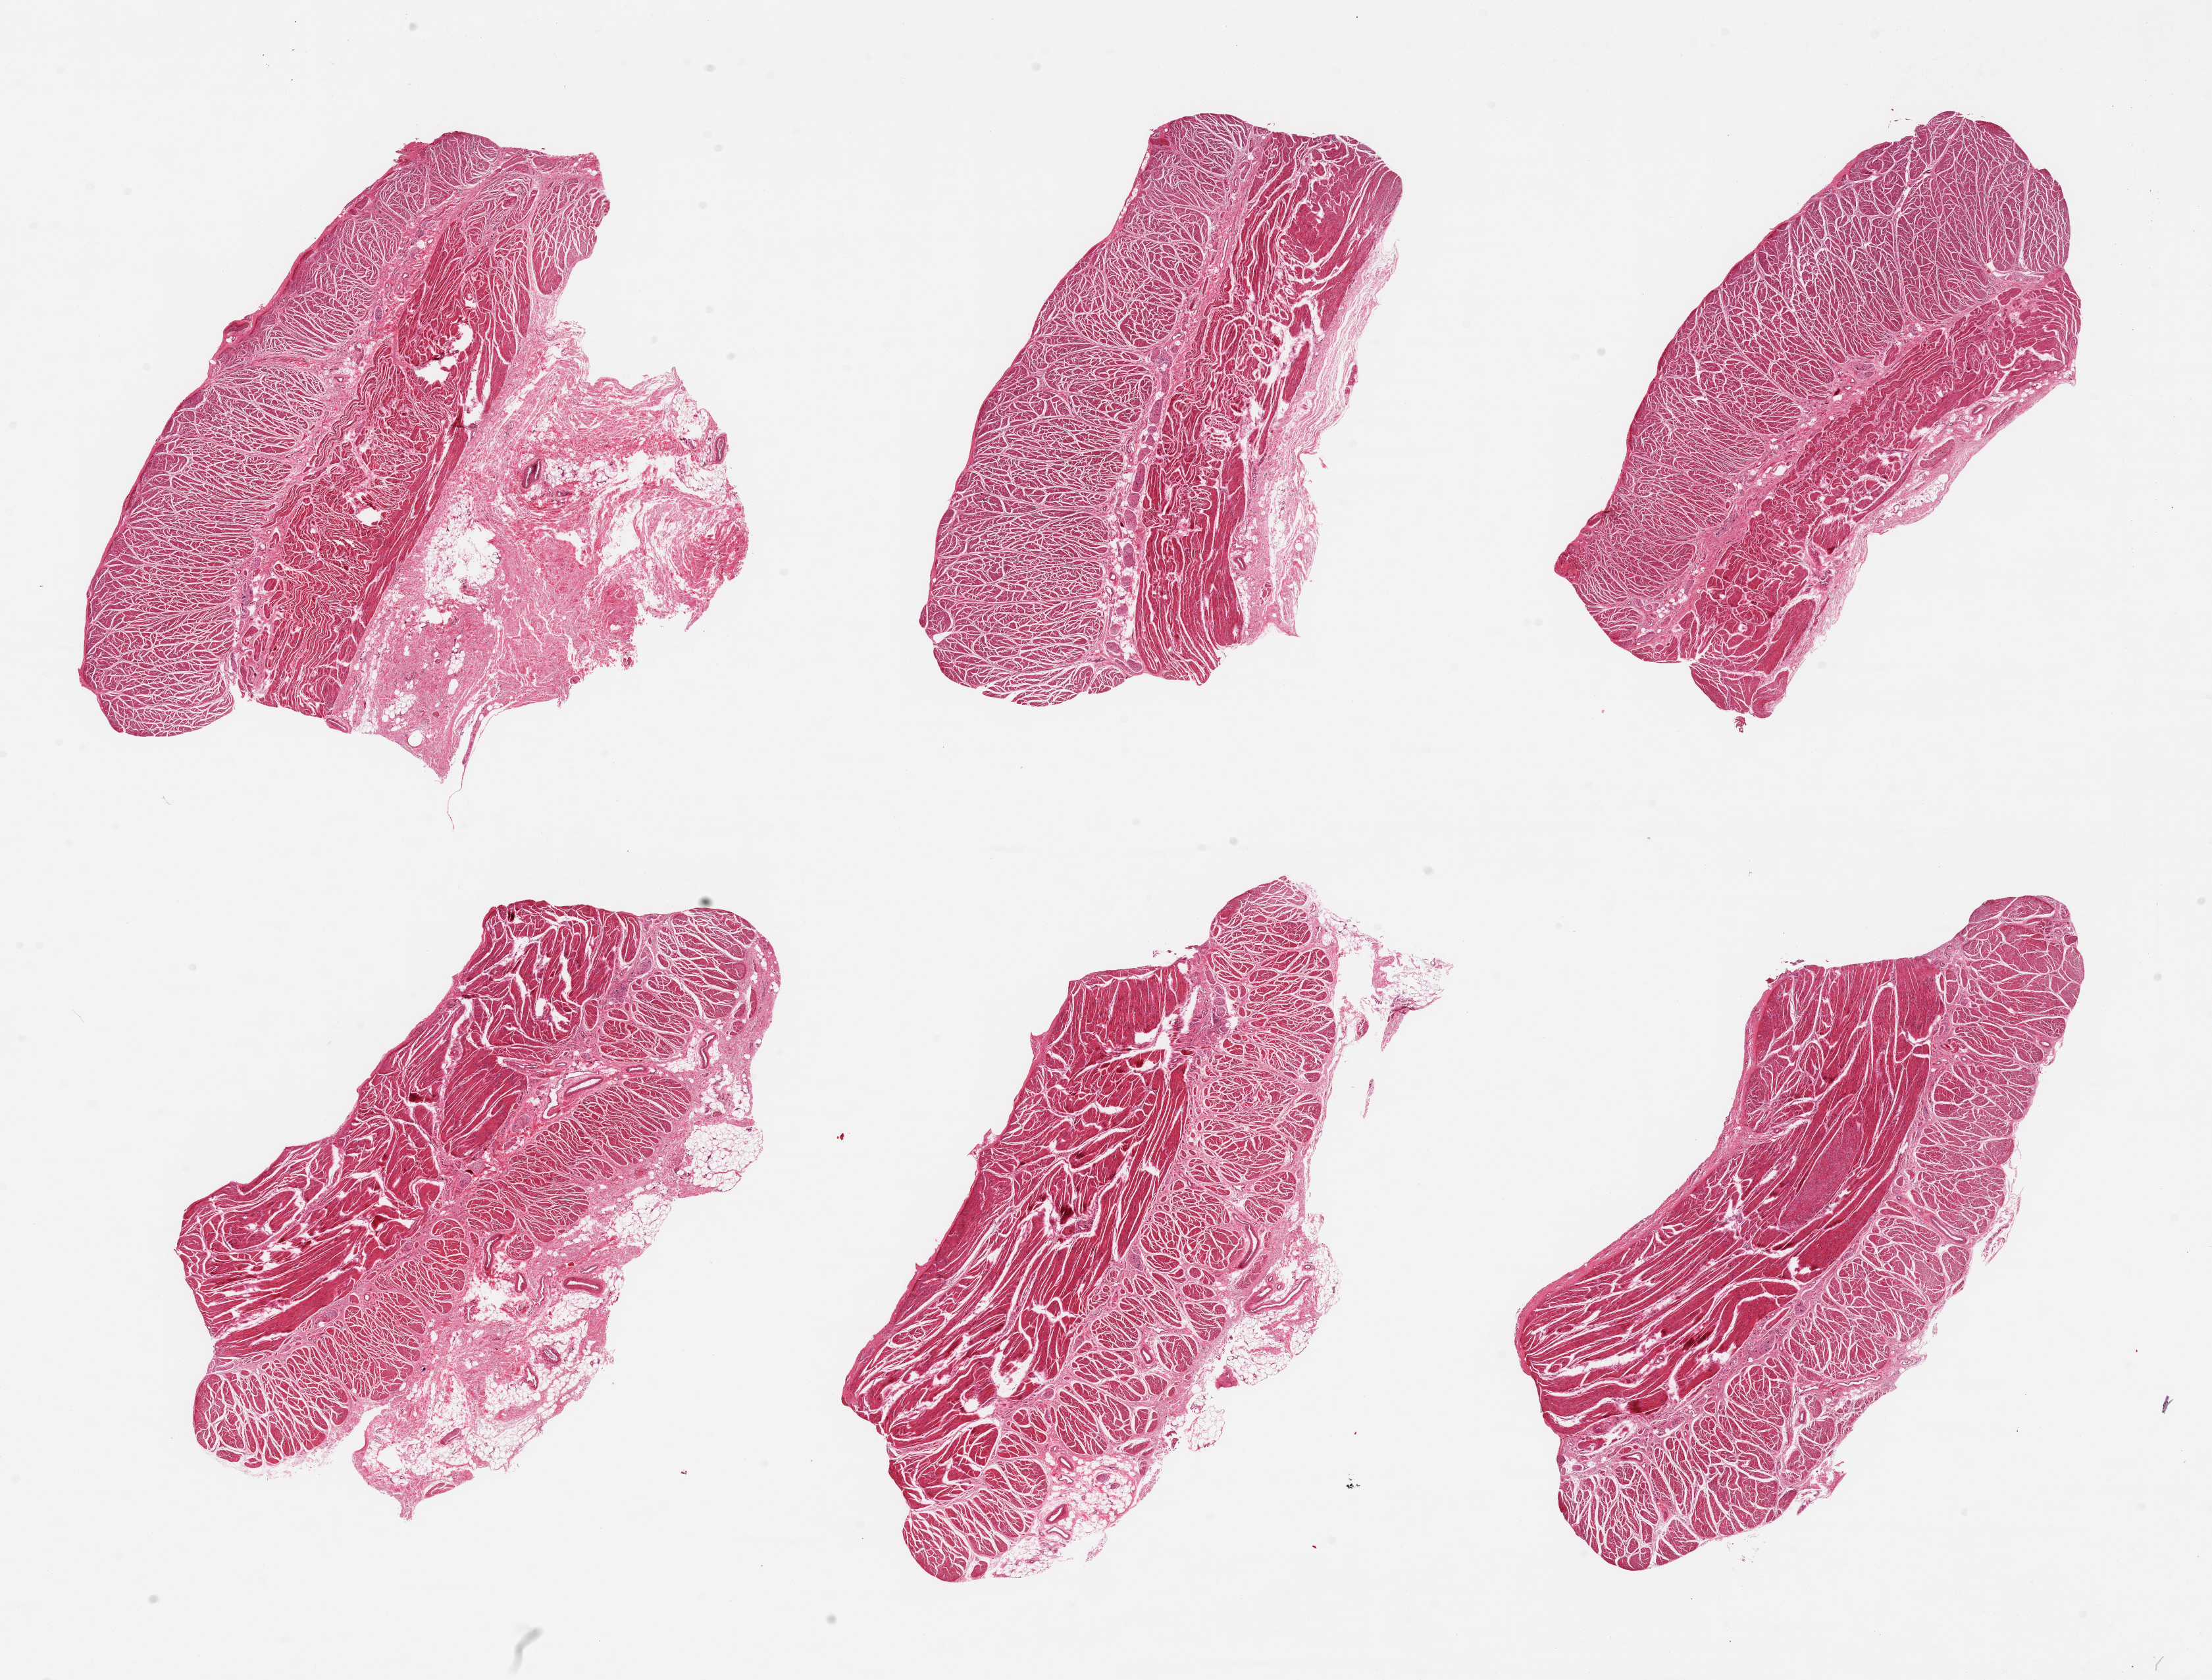
Digitized H&E-stained section — a low-resolution overview of the entire scanned area, about 26.6 x 20.2 mm (from a 20x scan), PAXgene-fixed, paraffin-embedded tissue, section of esophageal muscle (target tissue), tissue donor sample. Male donor.
- pathologist's review note for this sample: 6 pieces; target muscularis with attached serosa up to 3.5mm